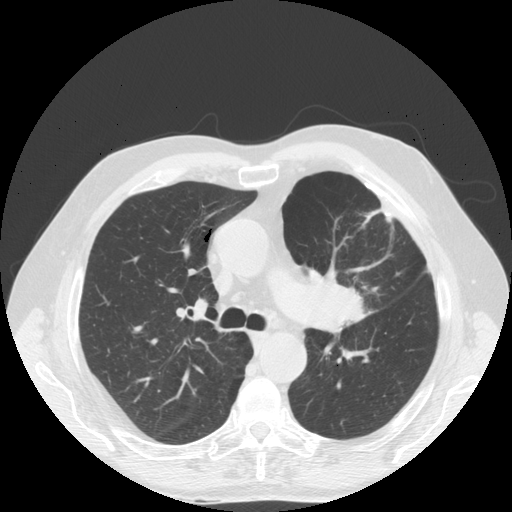
Axial slice from a low-dose chest CT screening exam, first (baseline) screen, lung window (W 1500 / L -600 HU), 2.5 mm slice thickness, standard (soft-tissue) reconstruction kernel (STANDARD). Male, age 70 years at enrolment. Former smoker at enrolment.
• Expert reader's lesion annotation, bounding box <291,255,382,344> (left, top, right, bottom; pixels).
• Screening reader's record for this exam (one nodule recorded; not confirmed to be the boxed lesion): non-calcified nodule or mass ≥4 mm, left upper lobe, 46 × 31 mm, spiculated (stellate) margins, soft tissue attenuation.